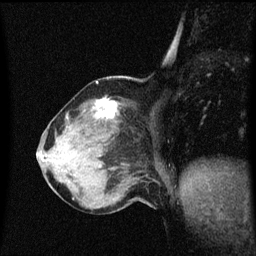
Breast MRI (dynamic contrast-enhanced), one sagittal slice; slice 21 of 60 in the series (ordered by position); dynamic contrast-enhanced series, image 2 of 3 at this slice position (ordered by acquisition); 1.5 T; TE 4.2 ms, TR 8.4 ms; 2 mm slice thickness; 256 × 256 image matrix. Patient: female, 64 years. From the clinical record (not read from this slice): setting: breast cancer imaged before/during neoadjuvant chemotherapy; receptor status: HR-positive, HER2-negative.
Outlined on this slice (semi-automatic segmentation, software-assisted and operator-edited):
- analysis volume of interest (the breast-tissue region the enhancement analysis was run in; not a lesion): box from (x=58, y=98) to (x=125, y=167) px
- tumour enhancement mask (voxels above the 70 % enhancement threshold inside the analysis volume of interest): (x=96, y=100)–(x=117, y=119)